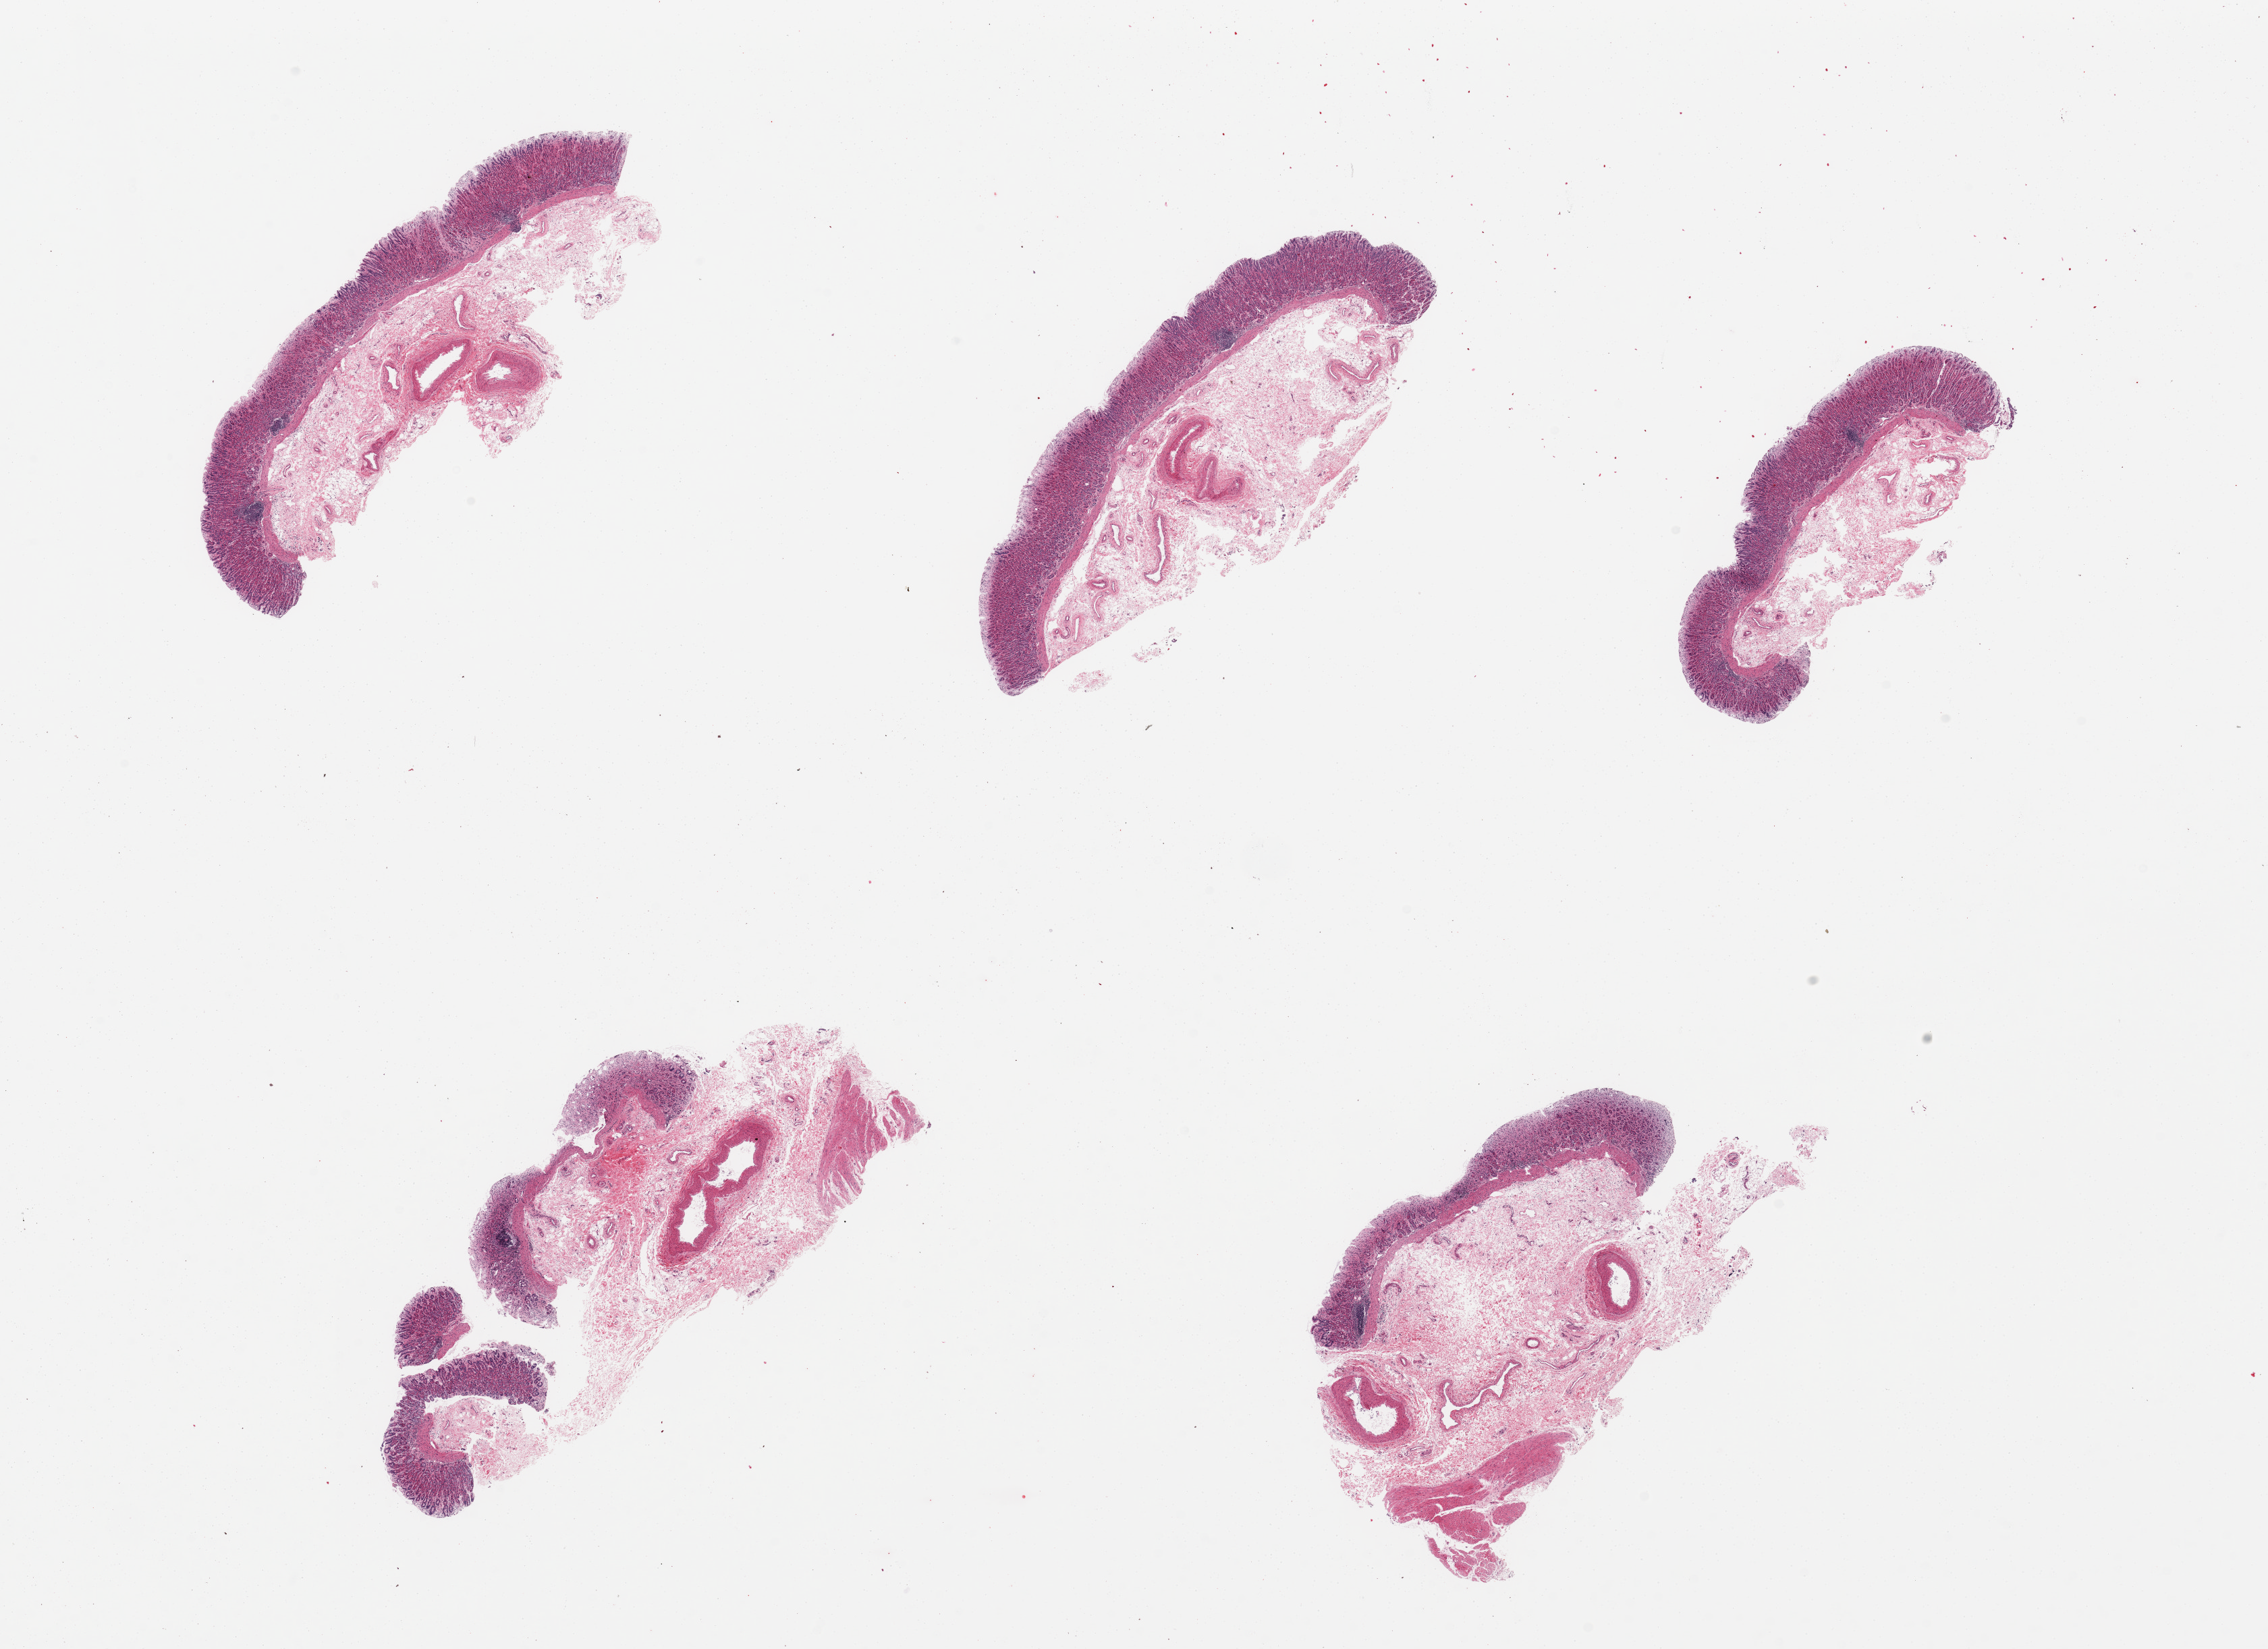
Haematoxylin and eosin whole-slide image, whole scanned area (about 26.6 x 19.3 mm) shown as a low-resolution overview. PAXgene-fixed paraffin-embedded (PFPE) section. Section of stomach (target tissue). Tissue donor sample. Donor sex: female.
* reviewer comment on this tissue sample: 5 pieces, predominantly autolysis rating of 1, focally 2; 2 of 5 pieces include portion of muscularis